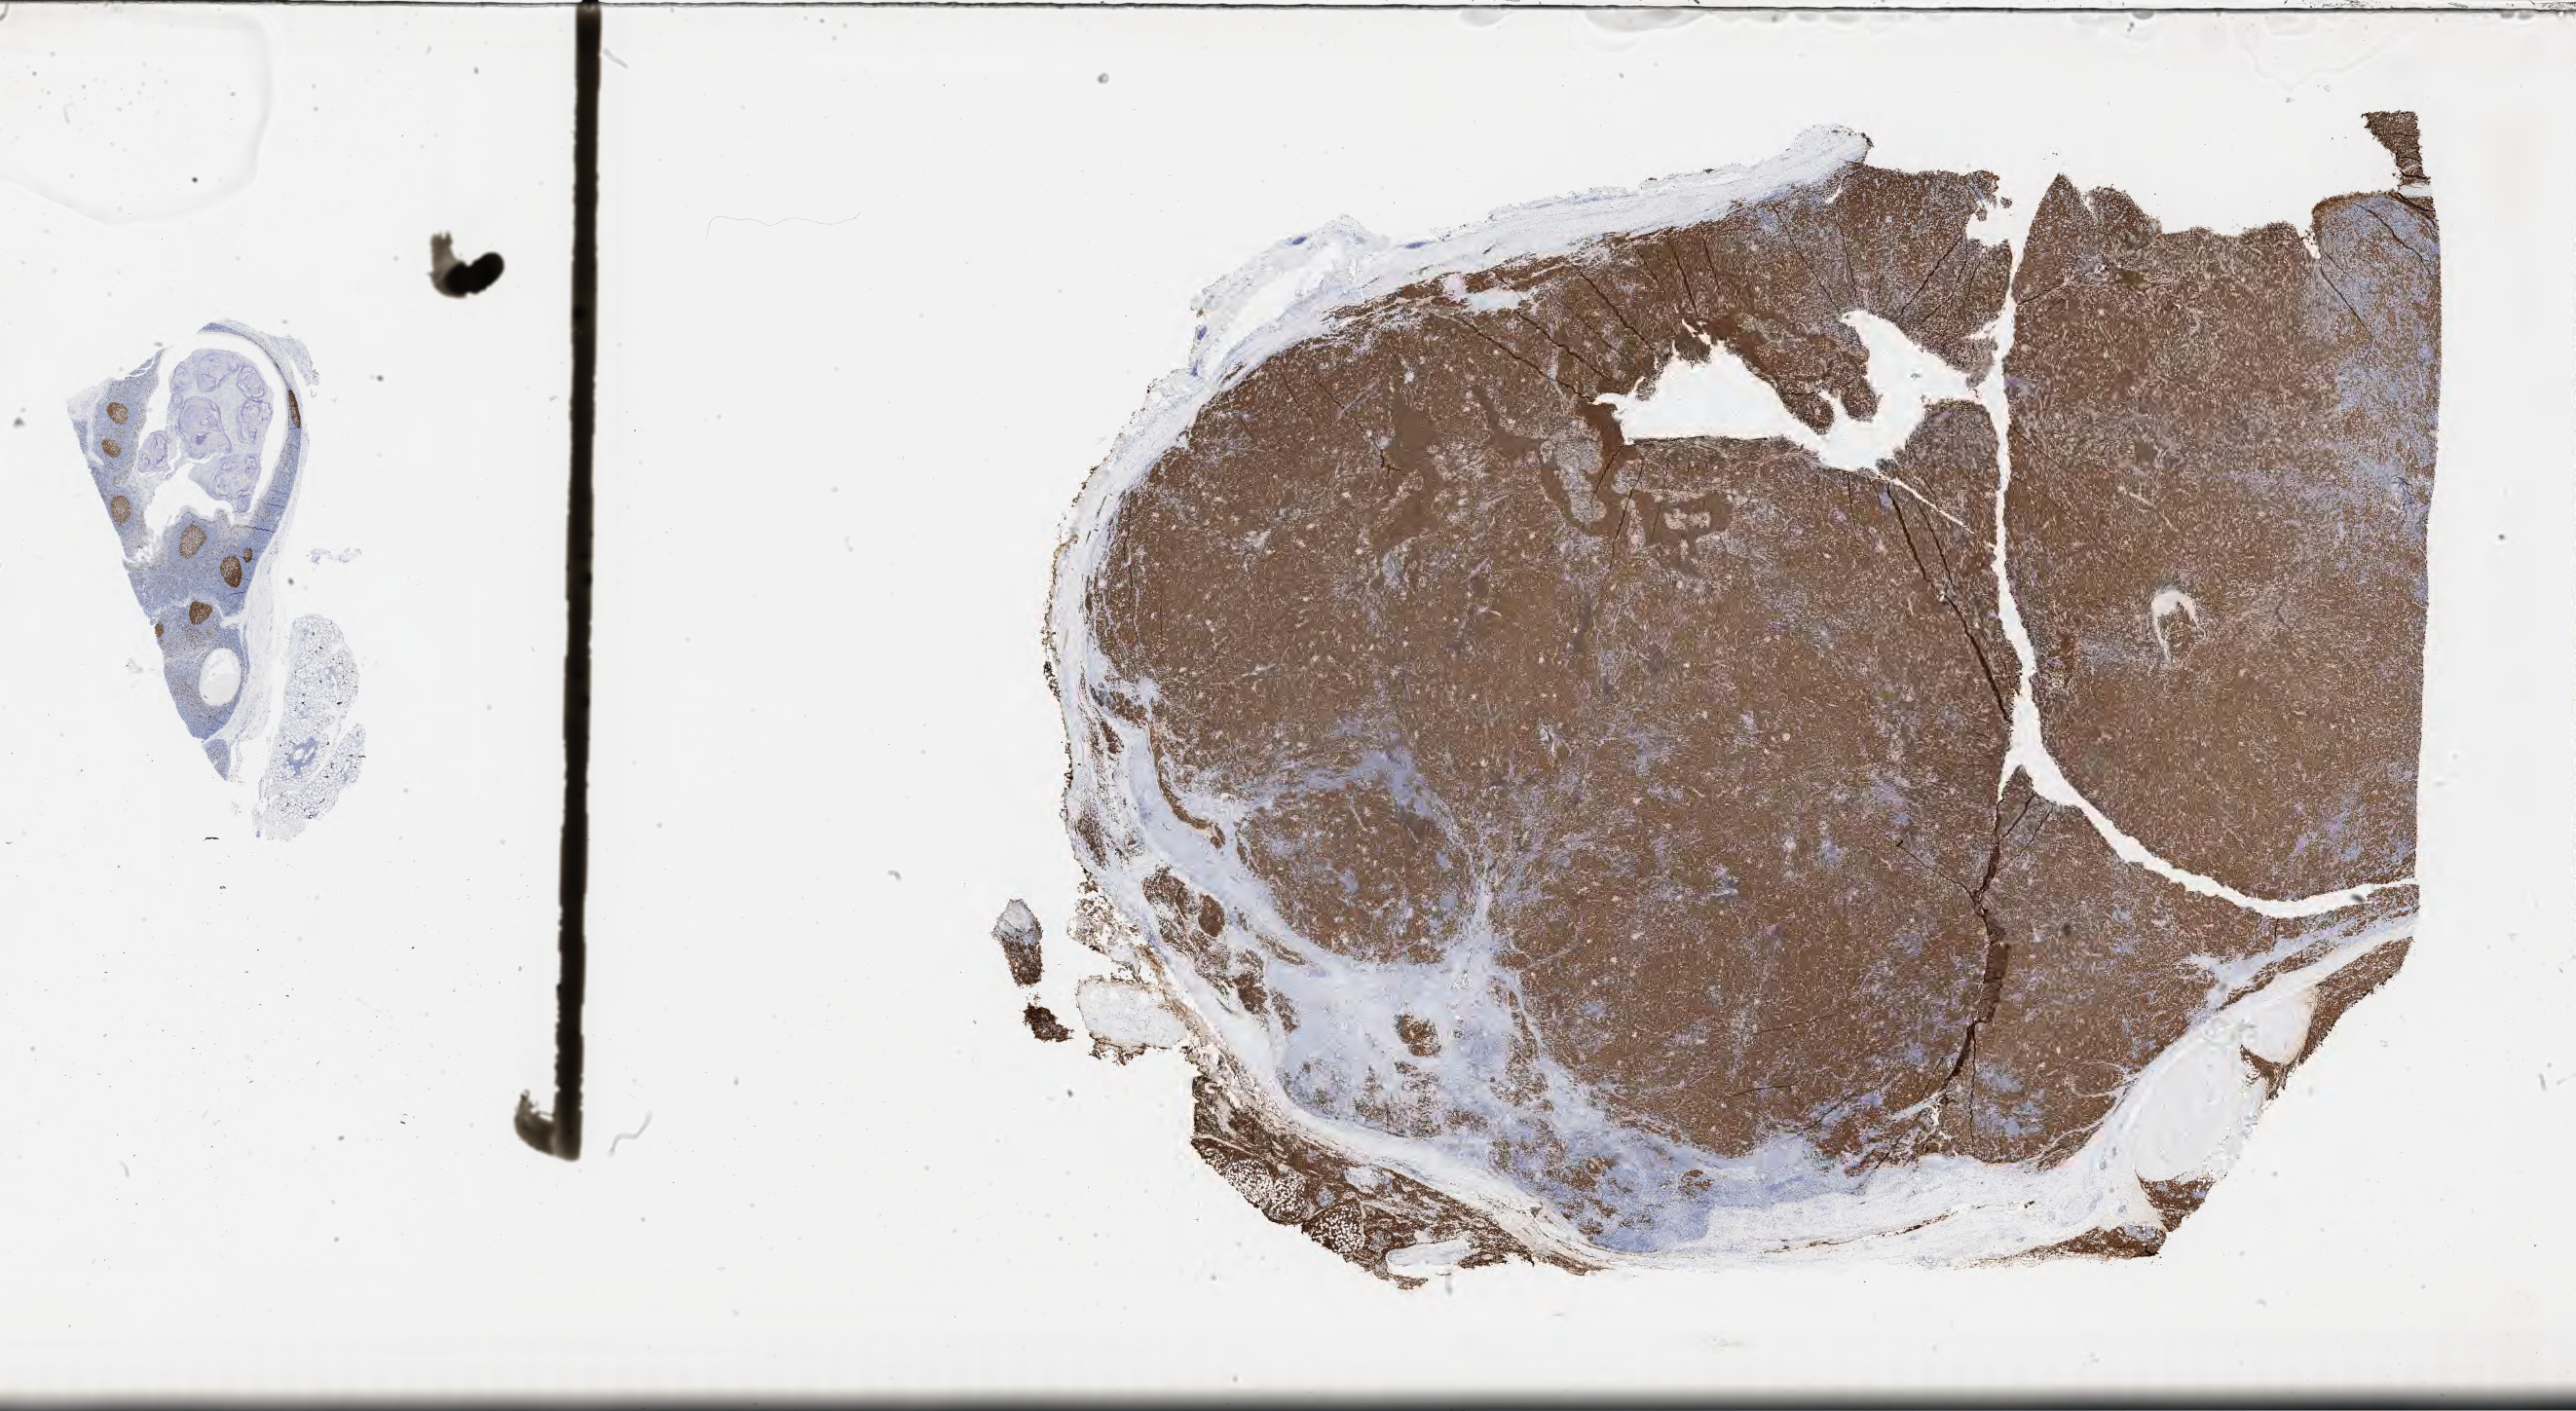
IHC for Ki-67, whole-slide image, a low-resolution overview of the entire scanned area, about 42.8 x 23.4 mm; specimen: tumor tissue. Male patient, 30 years old.
- diagnosis: Burkitt lymphoma, NOS